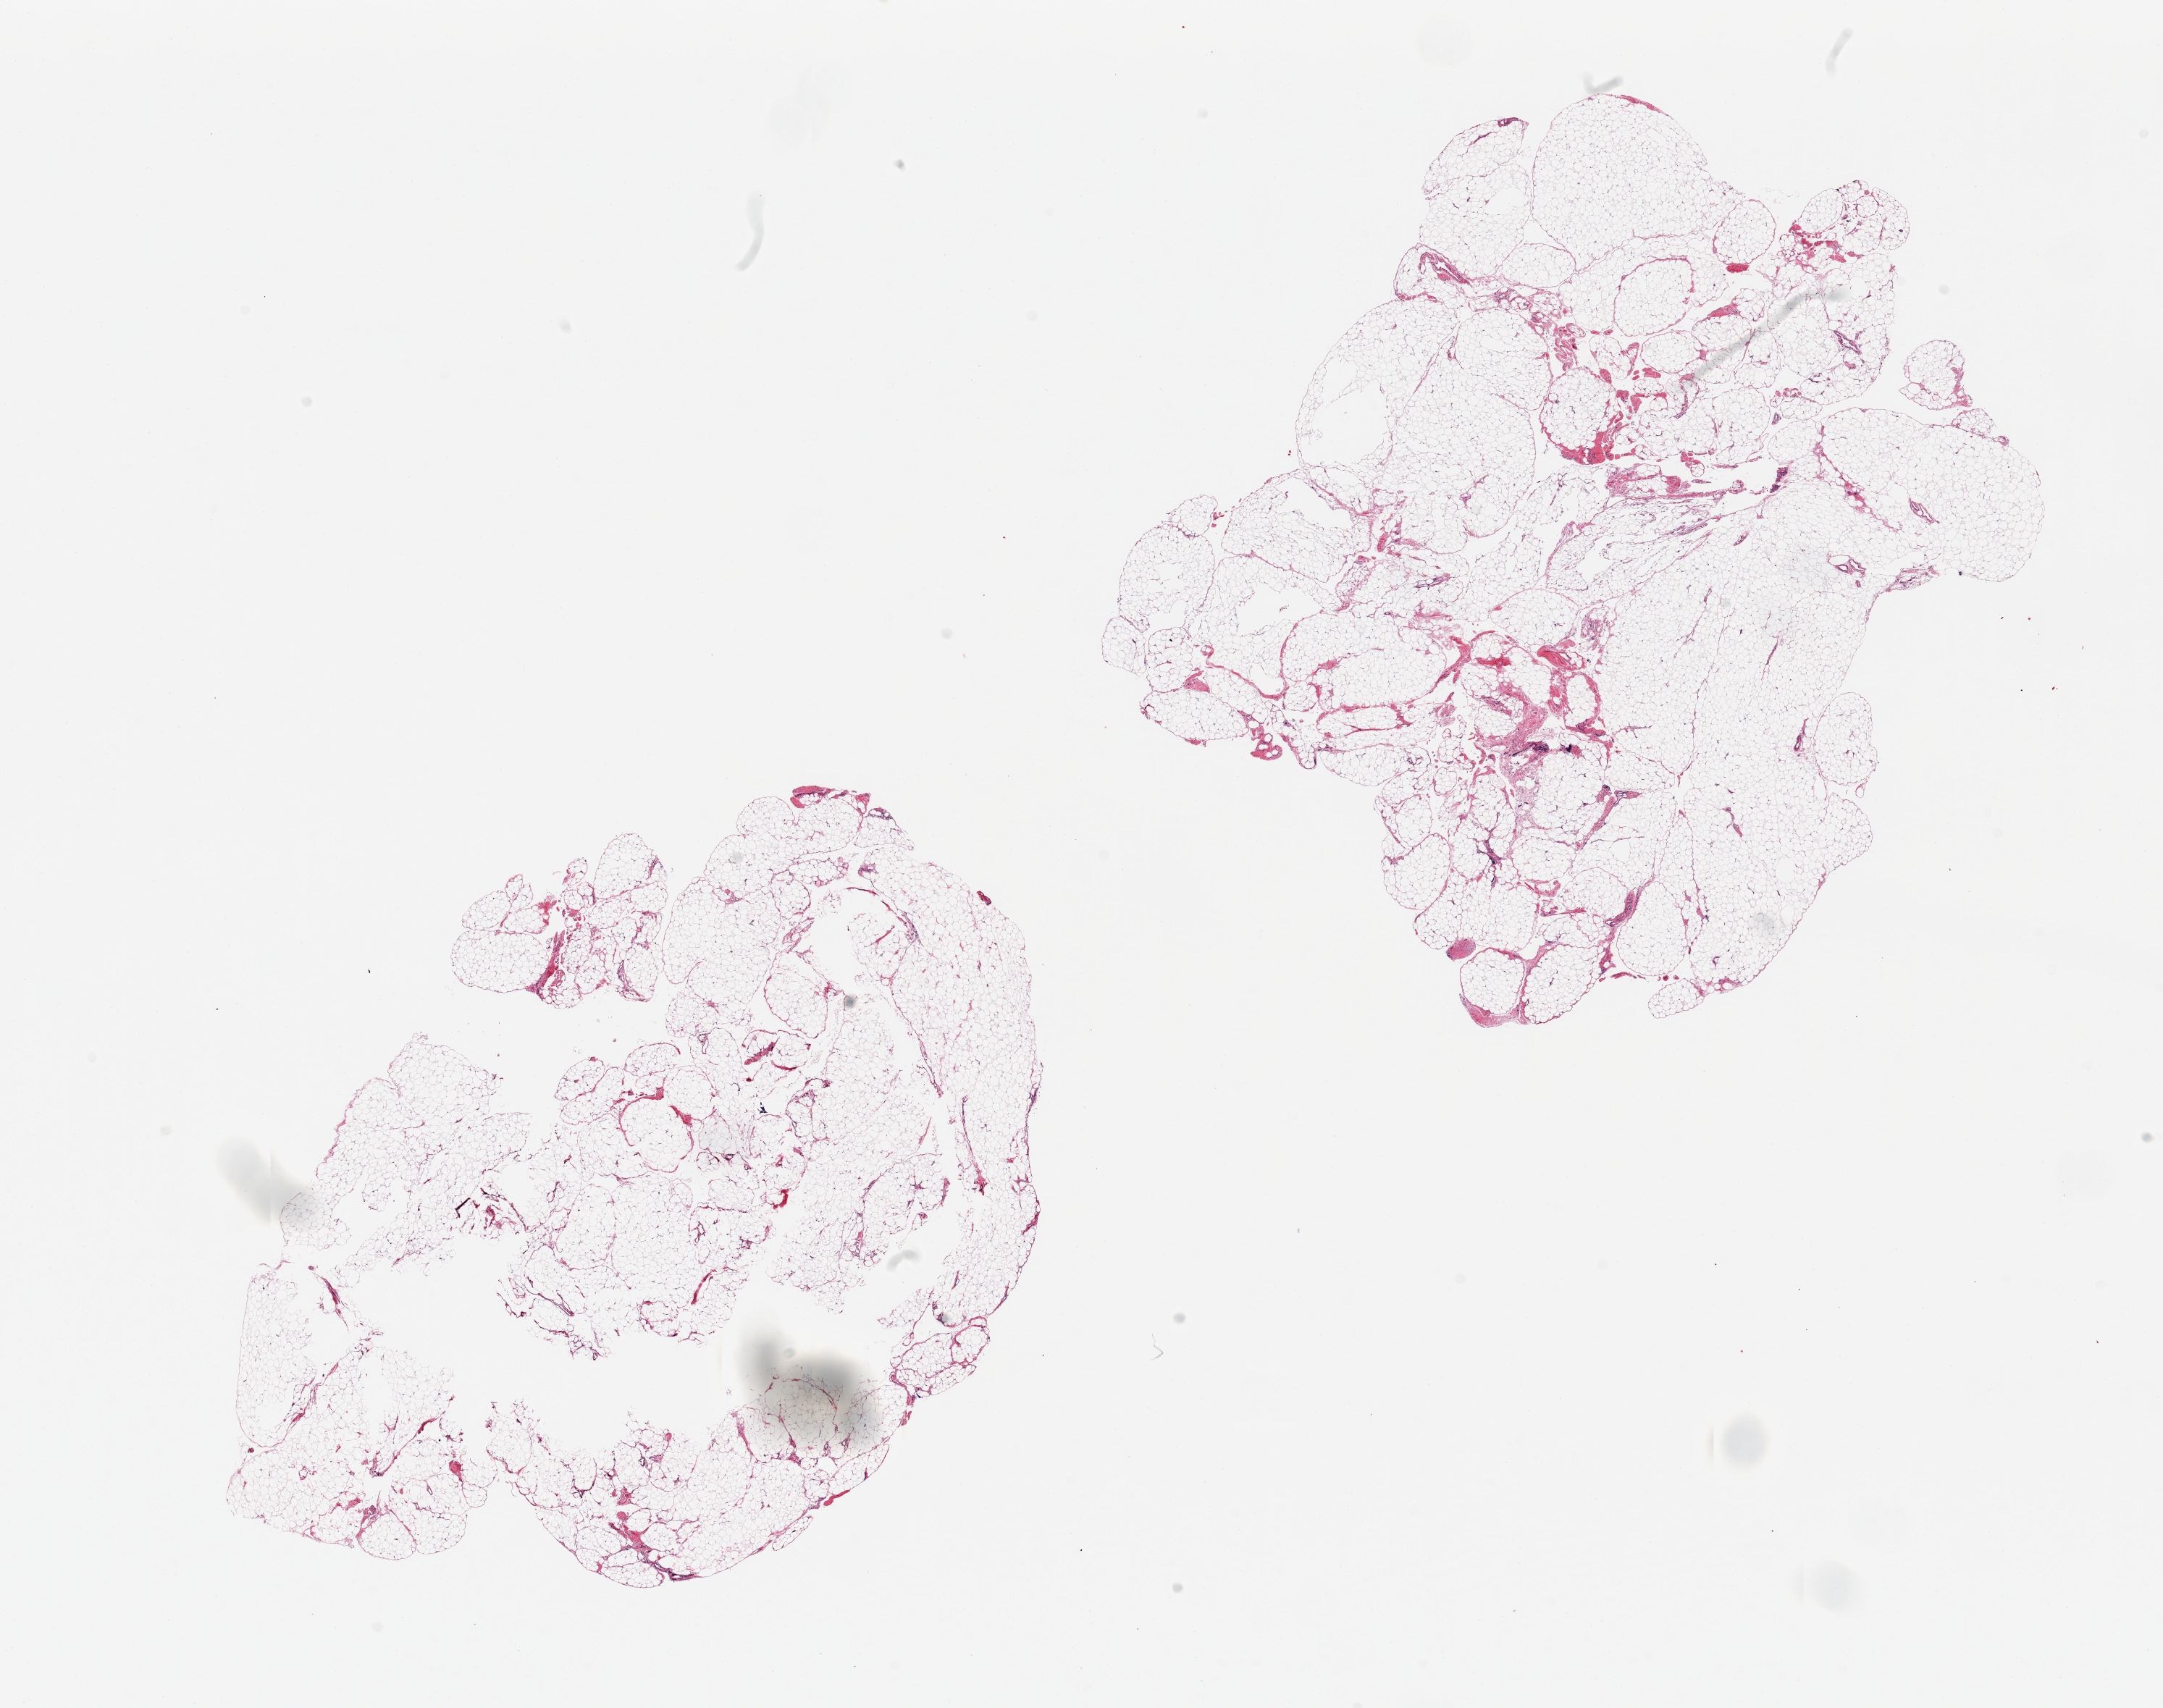
Whole-slide image, haematoxylin and eosin stain — low-resolution overview of the scanned area, about 23.6 x 18.7 mm (slide scanned at 20x); PAXgene-fixed, paraffin-embedded tissue; sampled site (target tissue): omentum; tissue donor sample. Donor: female.
Reviewer comment on this tissue sample: 2 pieces ~10x8mm.